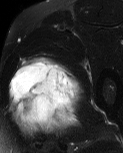
MRI of an extremity soft-tissue mass, one axial slice. Position 39 of 60 along the scan axis. T2-weighted fat-saturated. MR volume resampled by the dataset authors to the PET/CT grid (not the native acquisition matrix). 3.27 mm slice thickness. 123 × 153 image matrix. Male patient. From the clinical record (not read from this slice): histological type: pleiomorphic liposarcoma; grade: high; site of the primary tumour: left thigh.
Outlined on this slice (expert contour drawn on MRI and transferred to this co-registered scan by the dataset authors):
- gross tumour volume including surrounding oedema: bounding box (x1, y1, x2, y2) in pixels: (8, 54, 83, 140)
- gross tumour volume (mass): (11, 59, 78, 124)